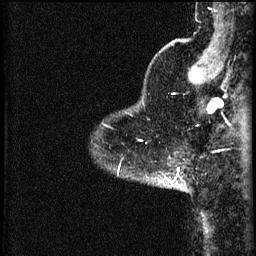
Breast MRI (dynamic contrast-enhanced), one sagittal slice. Position 8 of 60 along the scan axis. 3 images stored at this slice position (order not interpretable as contrast timing). 1.5 T. TE 4.2 ms, TR 8.2 ms. 2 mm slice thickness. 256 × 256 image matrix. Patient: female, 37 years.
Outlined on this slice (semi-automatic segmentation, software-assisted and operator-edited):
- analysis volume of interest (the breast-tissue region the enhancement analysis was run in; not a lesion): box from (x=148, y=168) to (x=187, y=191) px
- tumour enhancement mask (voxels above the 70 % enhancement threshold inside the analysis volume of interest): (x=168, y=168)–(x=179, y=183)